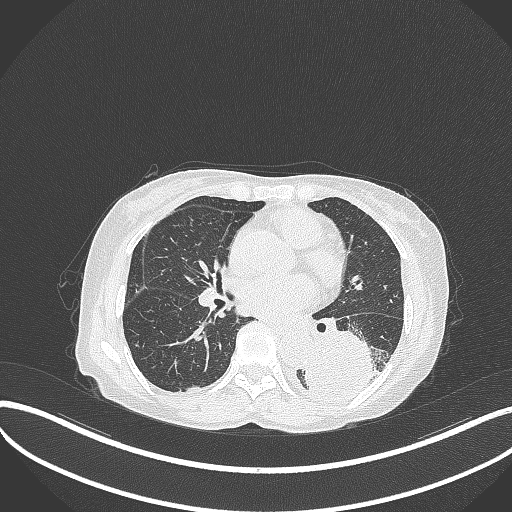
Chest CT, one axial slice; slice 148 of 370 in the series (ordered by position); 120 kVp; lung window (W 1500 / L -600 HU); 1 mm slice thickness; 512 × 512 image matrix. Patient: female, 78 years. From the clinical record (not read from this slice): clinical TNM (as recorded): T3 N0 M1.
Outlined on this slice (rectangle marked by the reading radiologist):
- lung tumour (recorded histology: squamous cell carcinoma): bounding box [x1, y1, x2, y2] px = [305, 329, 387, 403]